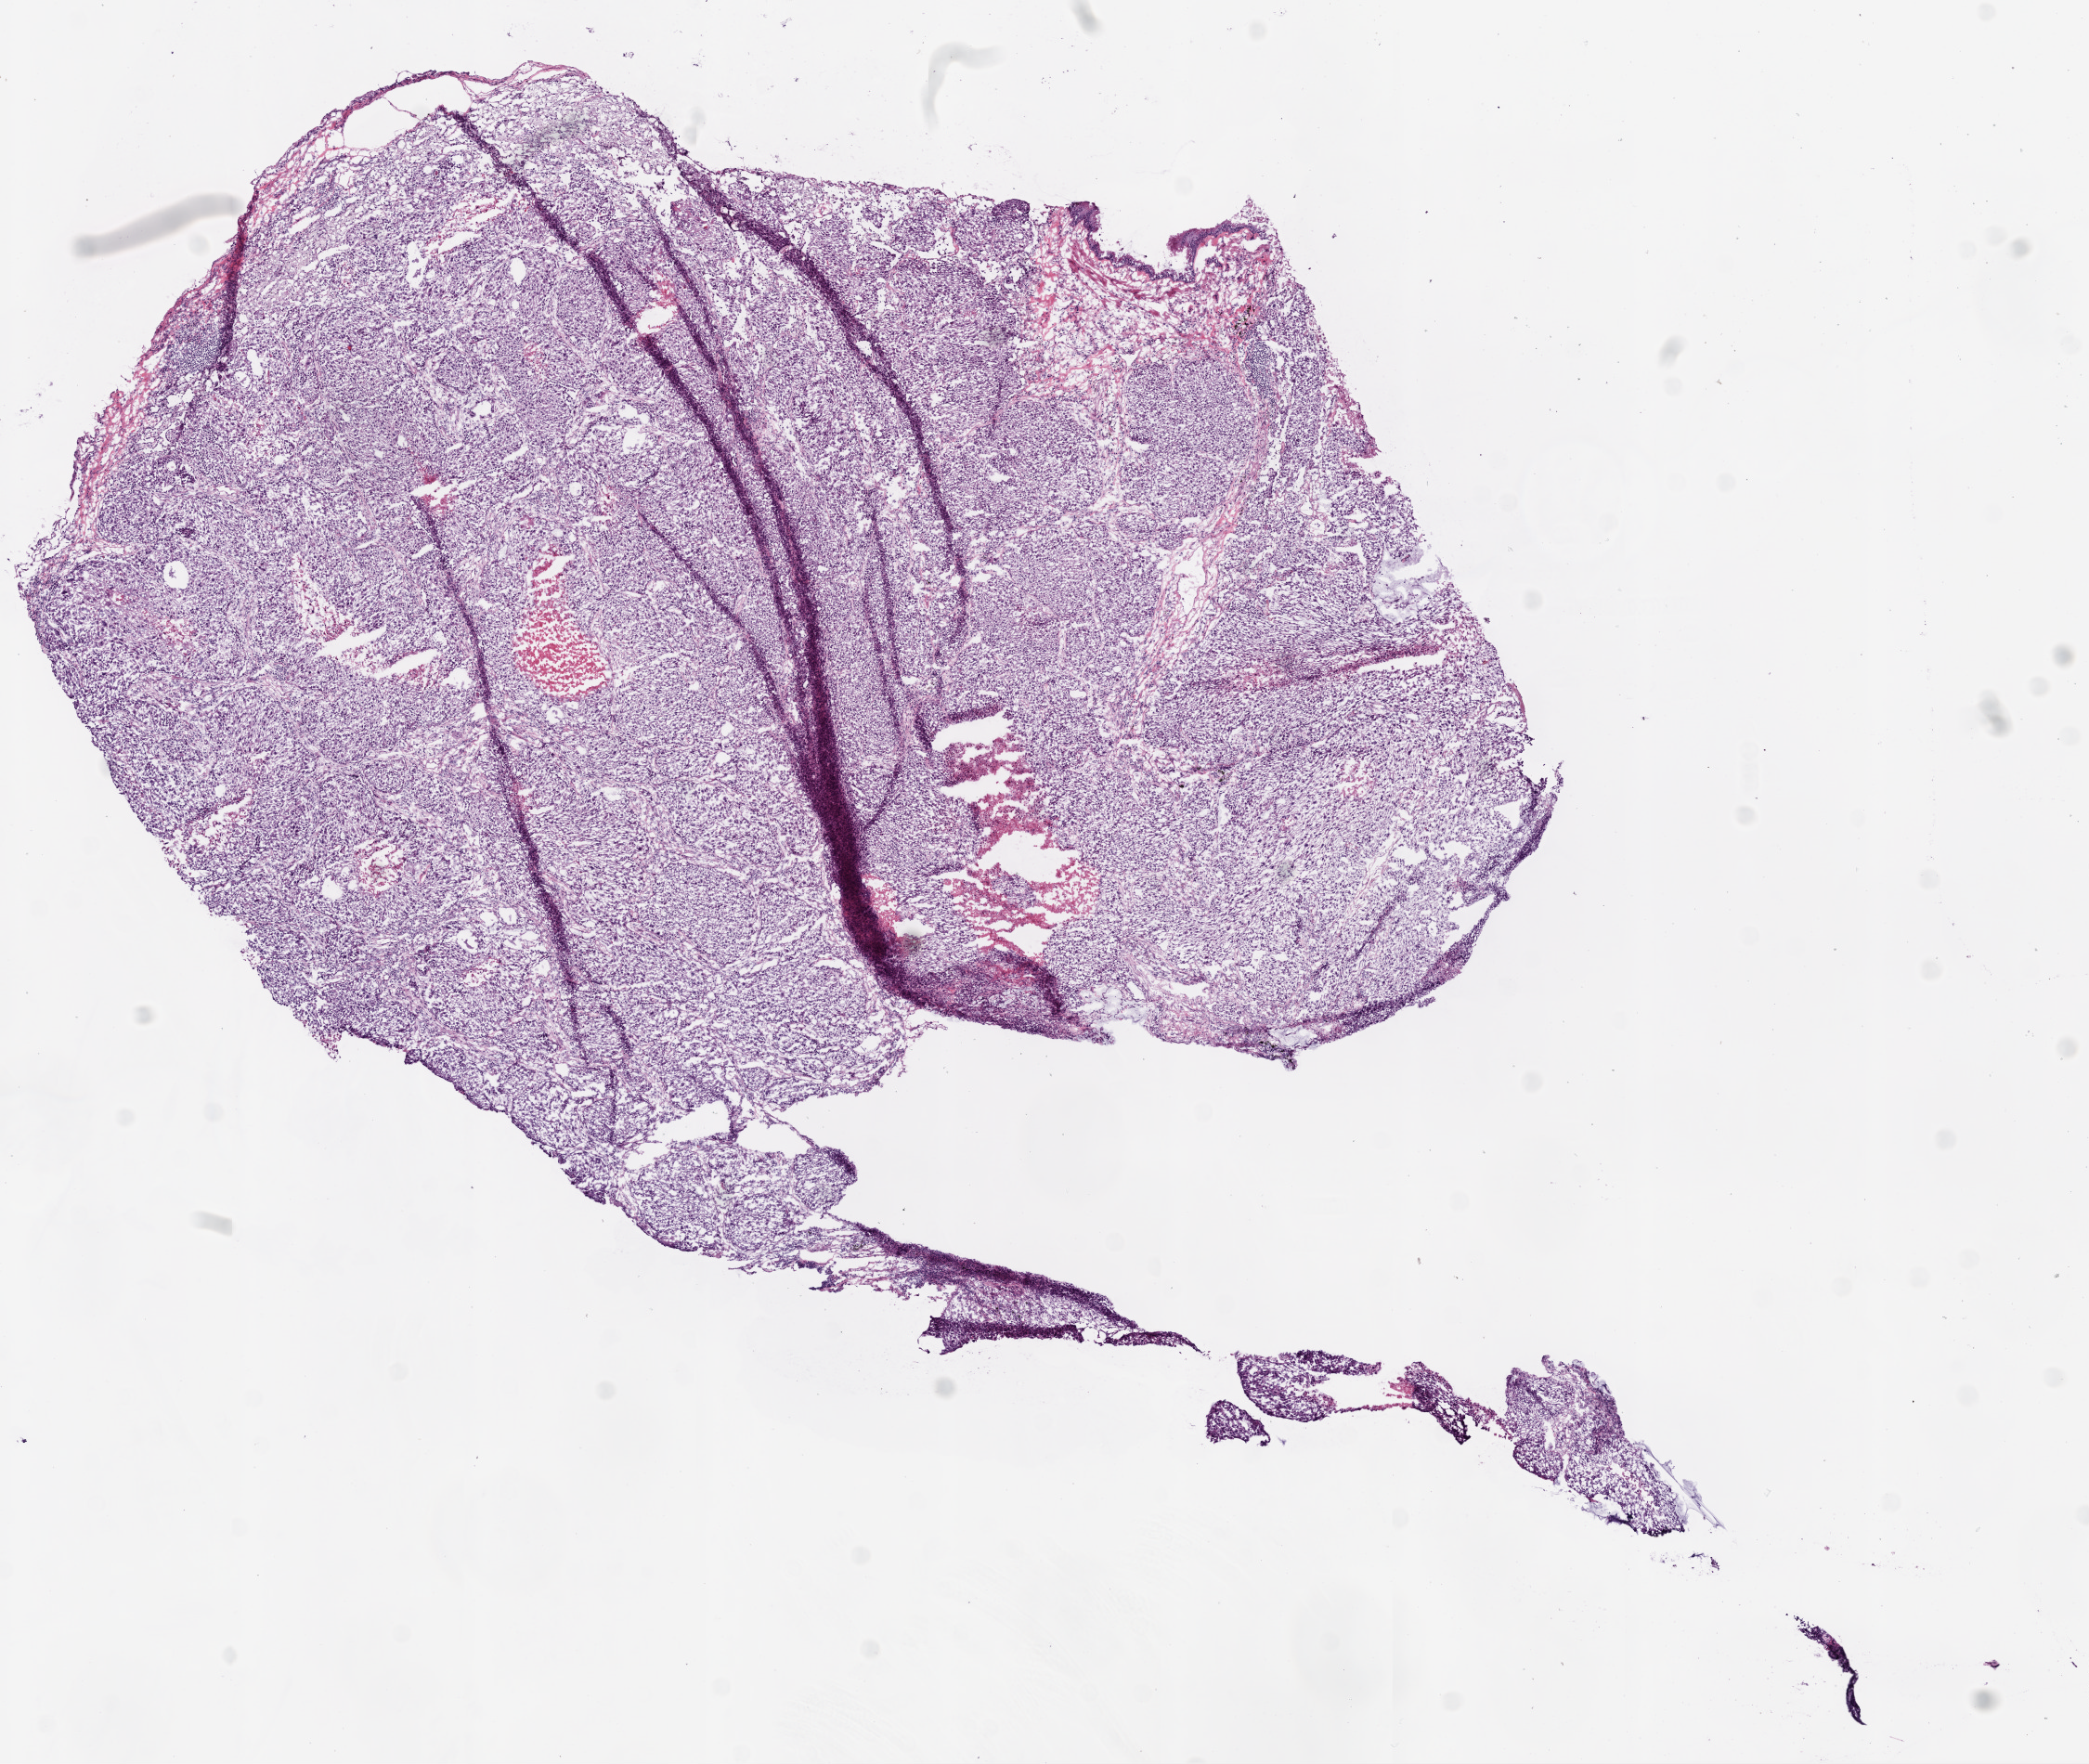
Digitized H&E-stained tissue section (whole slide), shown as a low-resolution overview of the whole scanned area (about 9.0 x 7.6 mm); frozen section from the bottom of the tissue portion; primary tumour sample from the lung. Patient: female, age at initial diagnosis 68 years. Composition of this section per pathologist review: tumour cells 88%, tumour nuclei 85%, normal cells 2%, stromal cells 5%, necrosis 5%.
Laterality: right. Pathologic diagnosis: Squamous cell carcinoma, NOS (upper lobe, lung). AJCC pathologic stage: IA (5th edition).